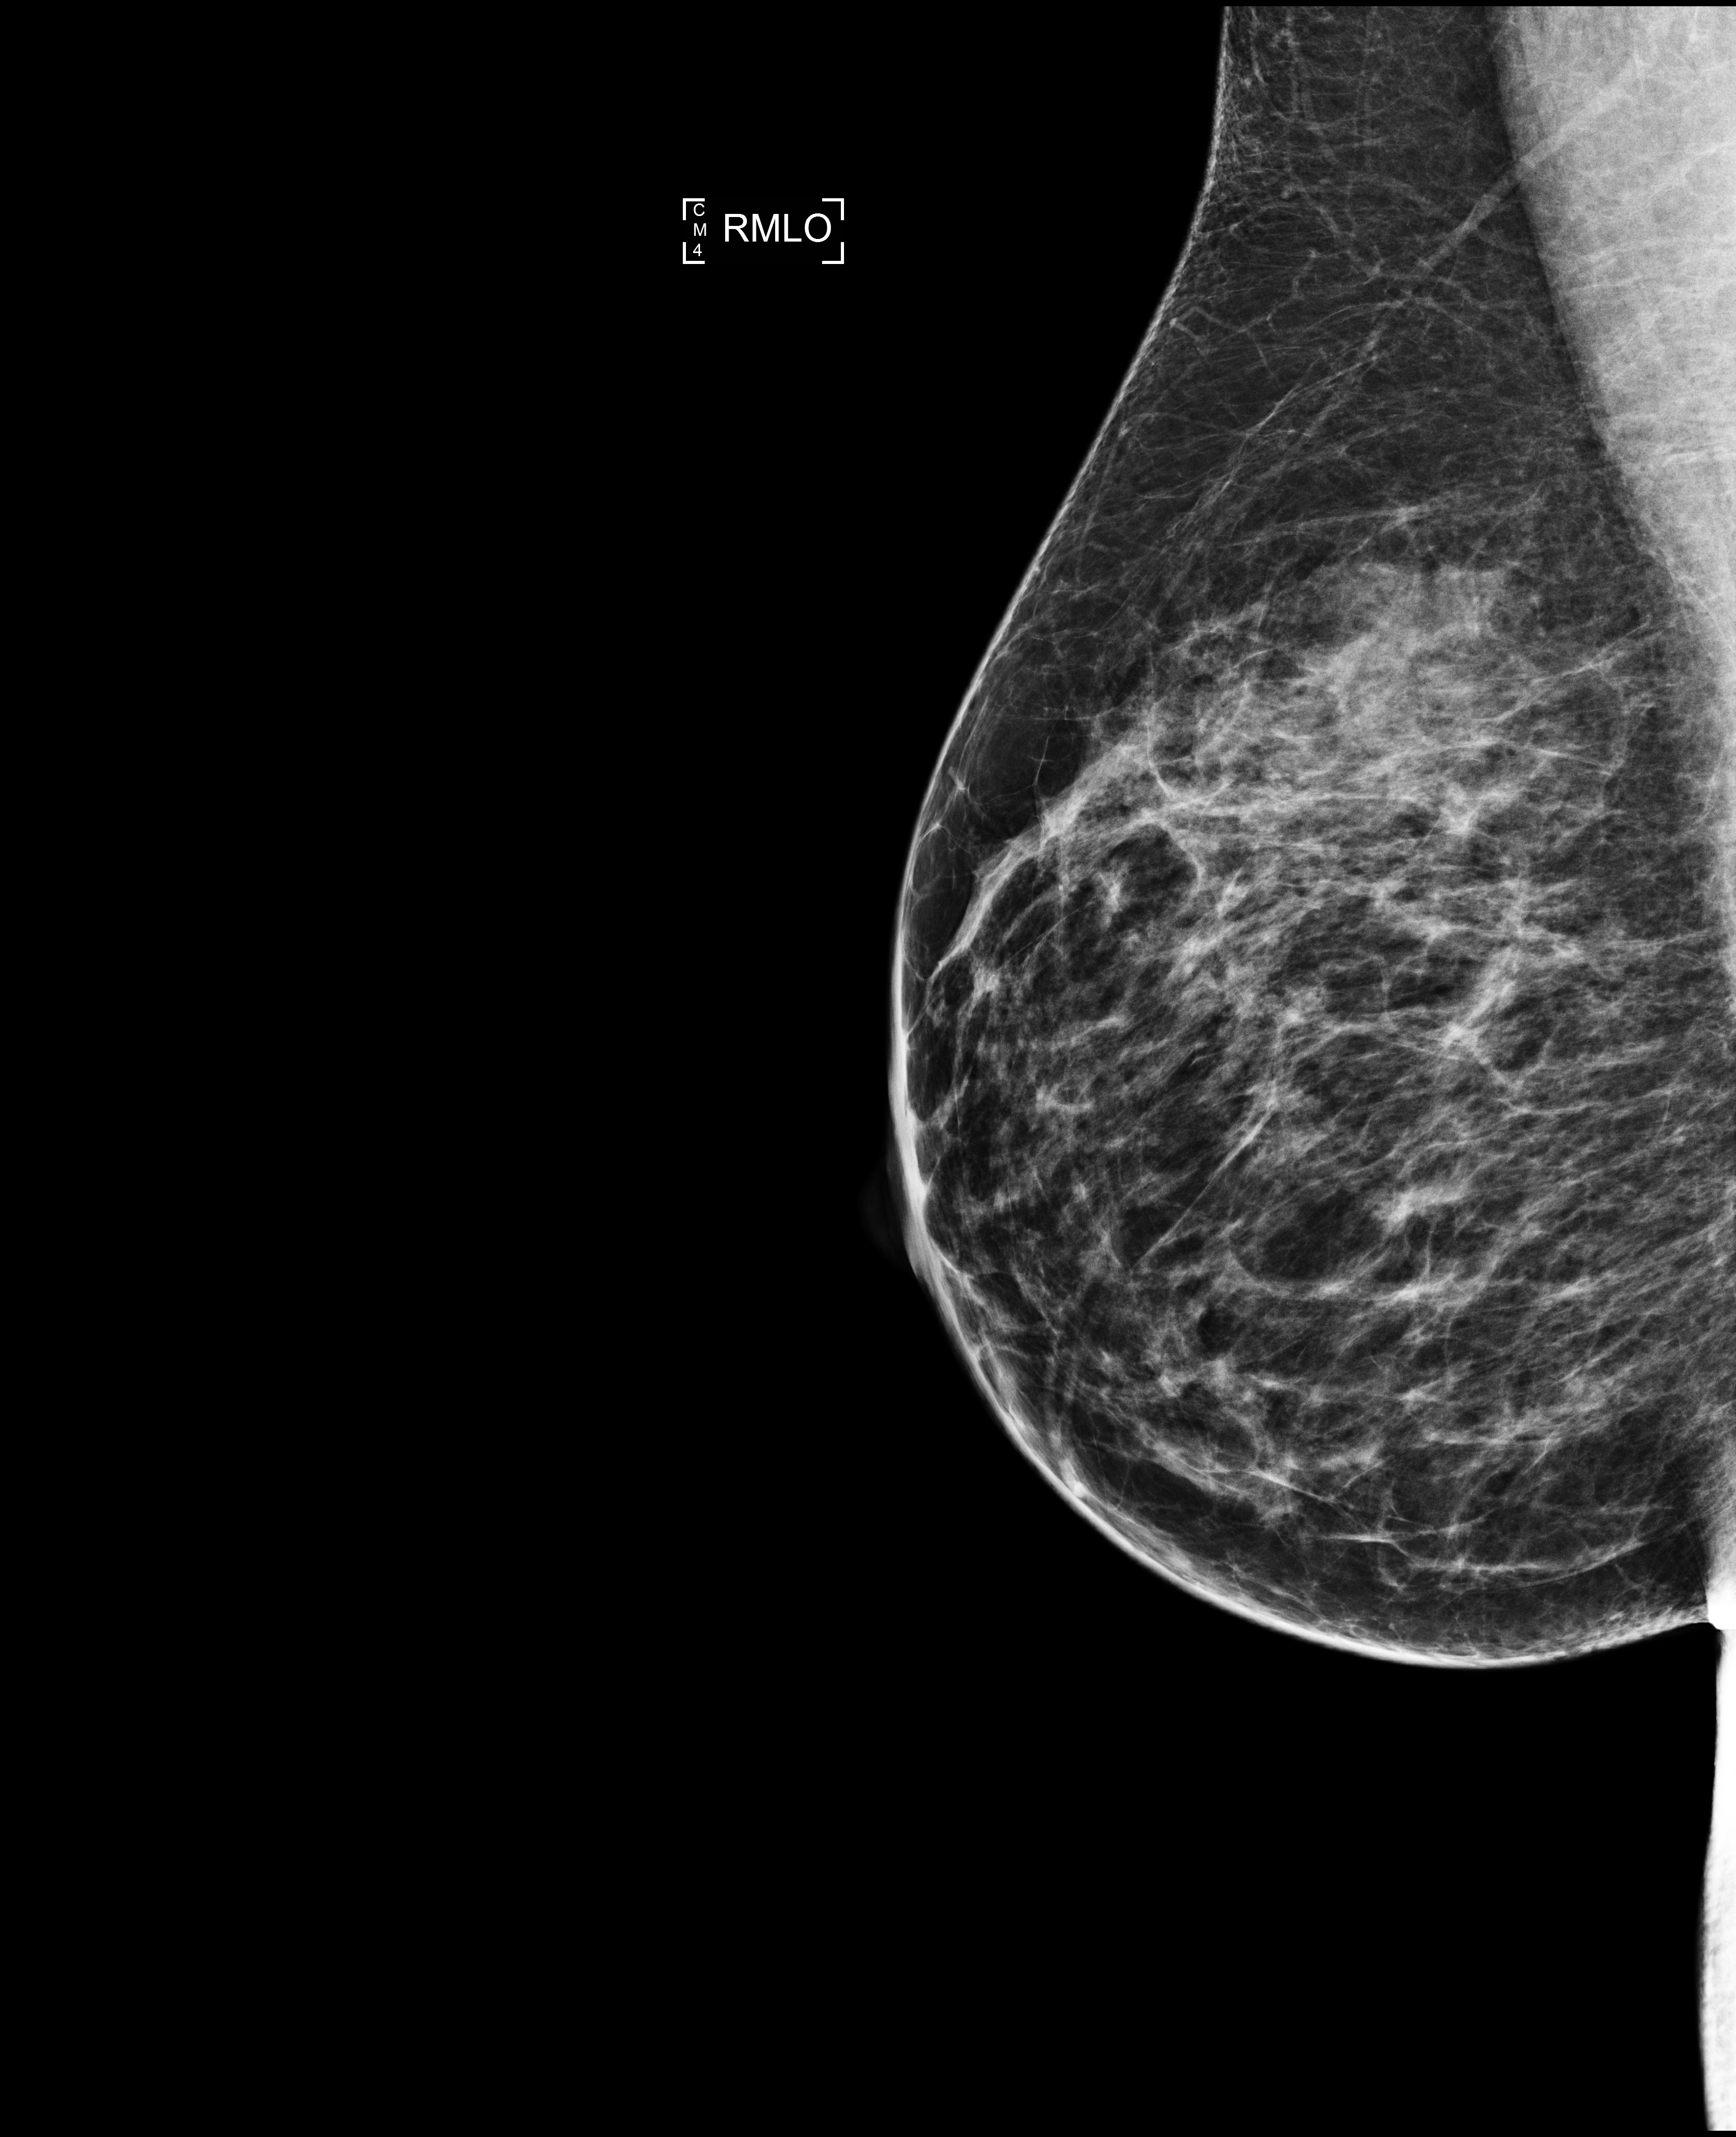
Digital mammogram (FFDM), right breast, MLO view, annual screening mammography examination. Patient aged 46 years (female).
Breast density at the screening exam (both breasts): heterogeneously dense (BI-RADS density category c). Final BI-RADS assessment for this screening round (tomosynthesis exam, both breasts): category 1. Recall: no recall after this screen.